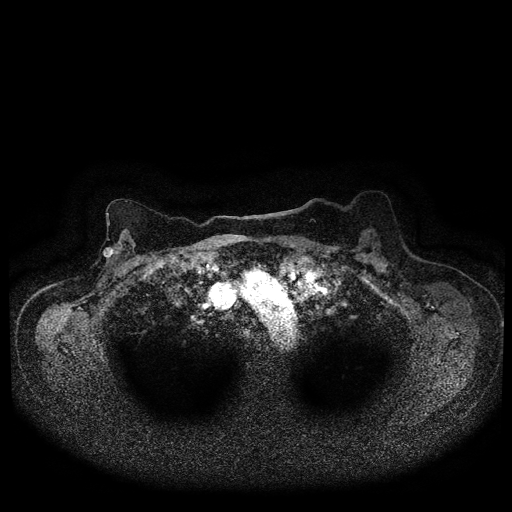
Breast MRI (dynamic contrast-enhanced, multi-phase), one axial slice. Position 73 of 116 along the scan axis. Dynamic contrast-enhanced series, time point 2 of 5 at this slice position (early post-contrast). 1.5 T. TE 2.7 ms, TR 5.4 ms. 2 mm slice thickness. 512 × 512 image matrix. Patient: female, 72 years.
Structures marked on this image (semi-automatic segmentation, software-assisted and operator-edited):
- breast lesion (labelled 'tumour' in the annotation; benign lesions carry a separate 'benign' label): box from (x=101, y=246) to (x=116, y=259) px